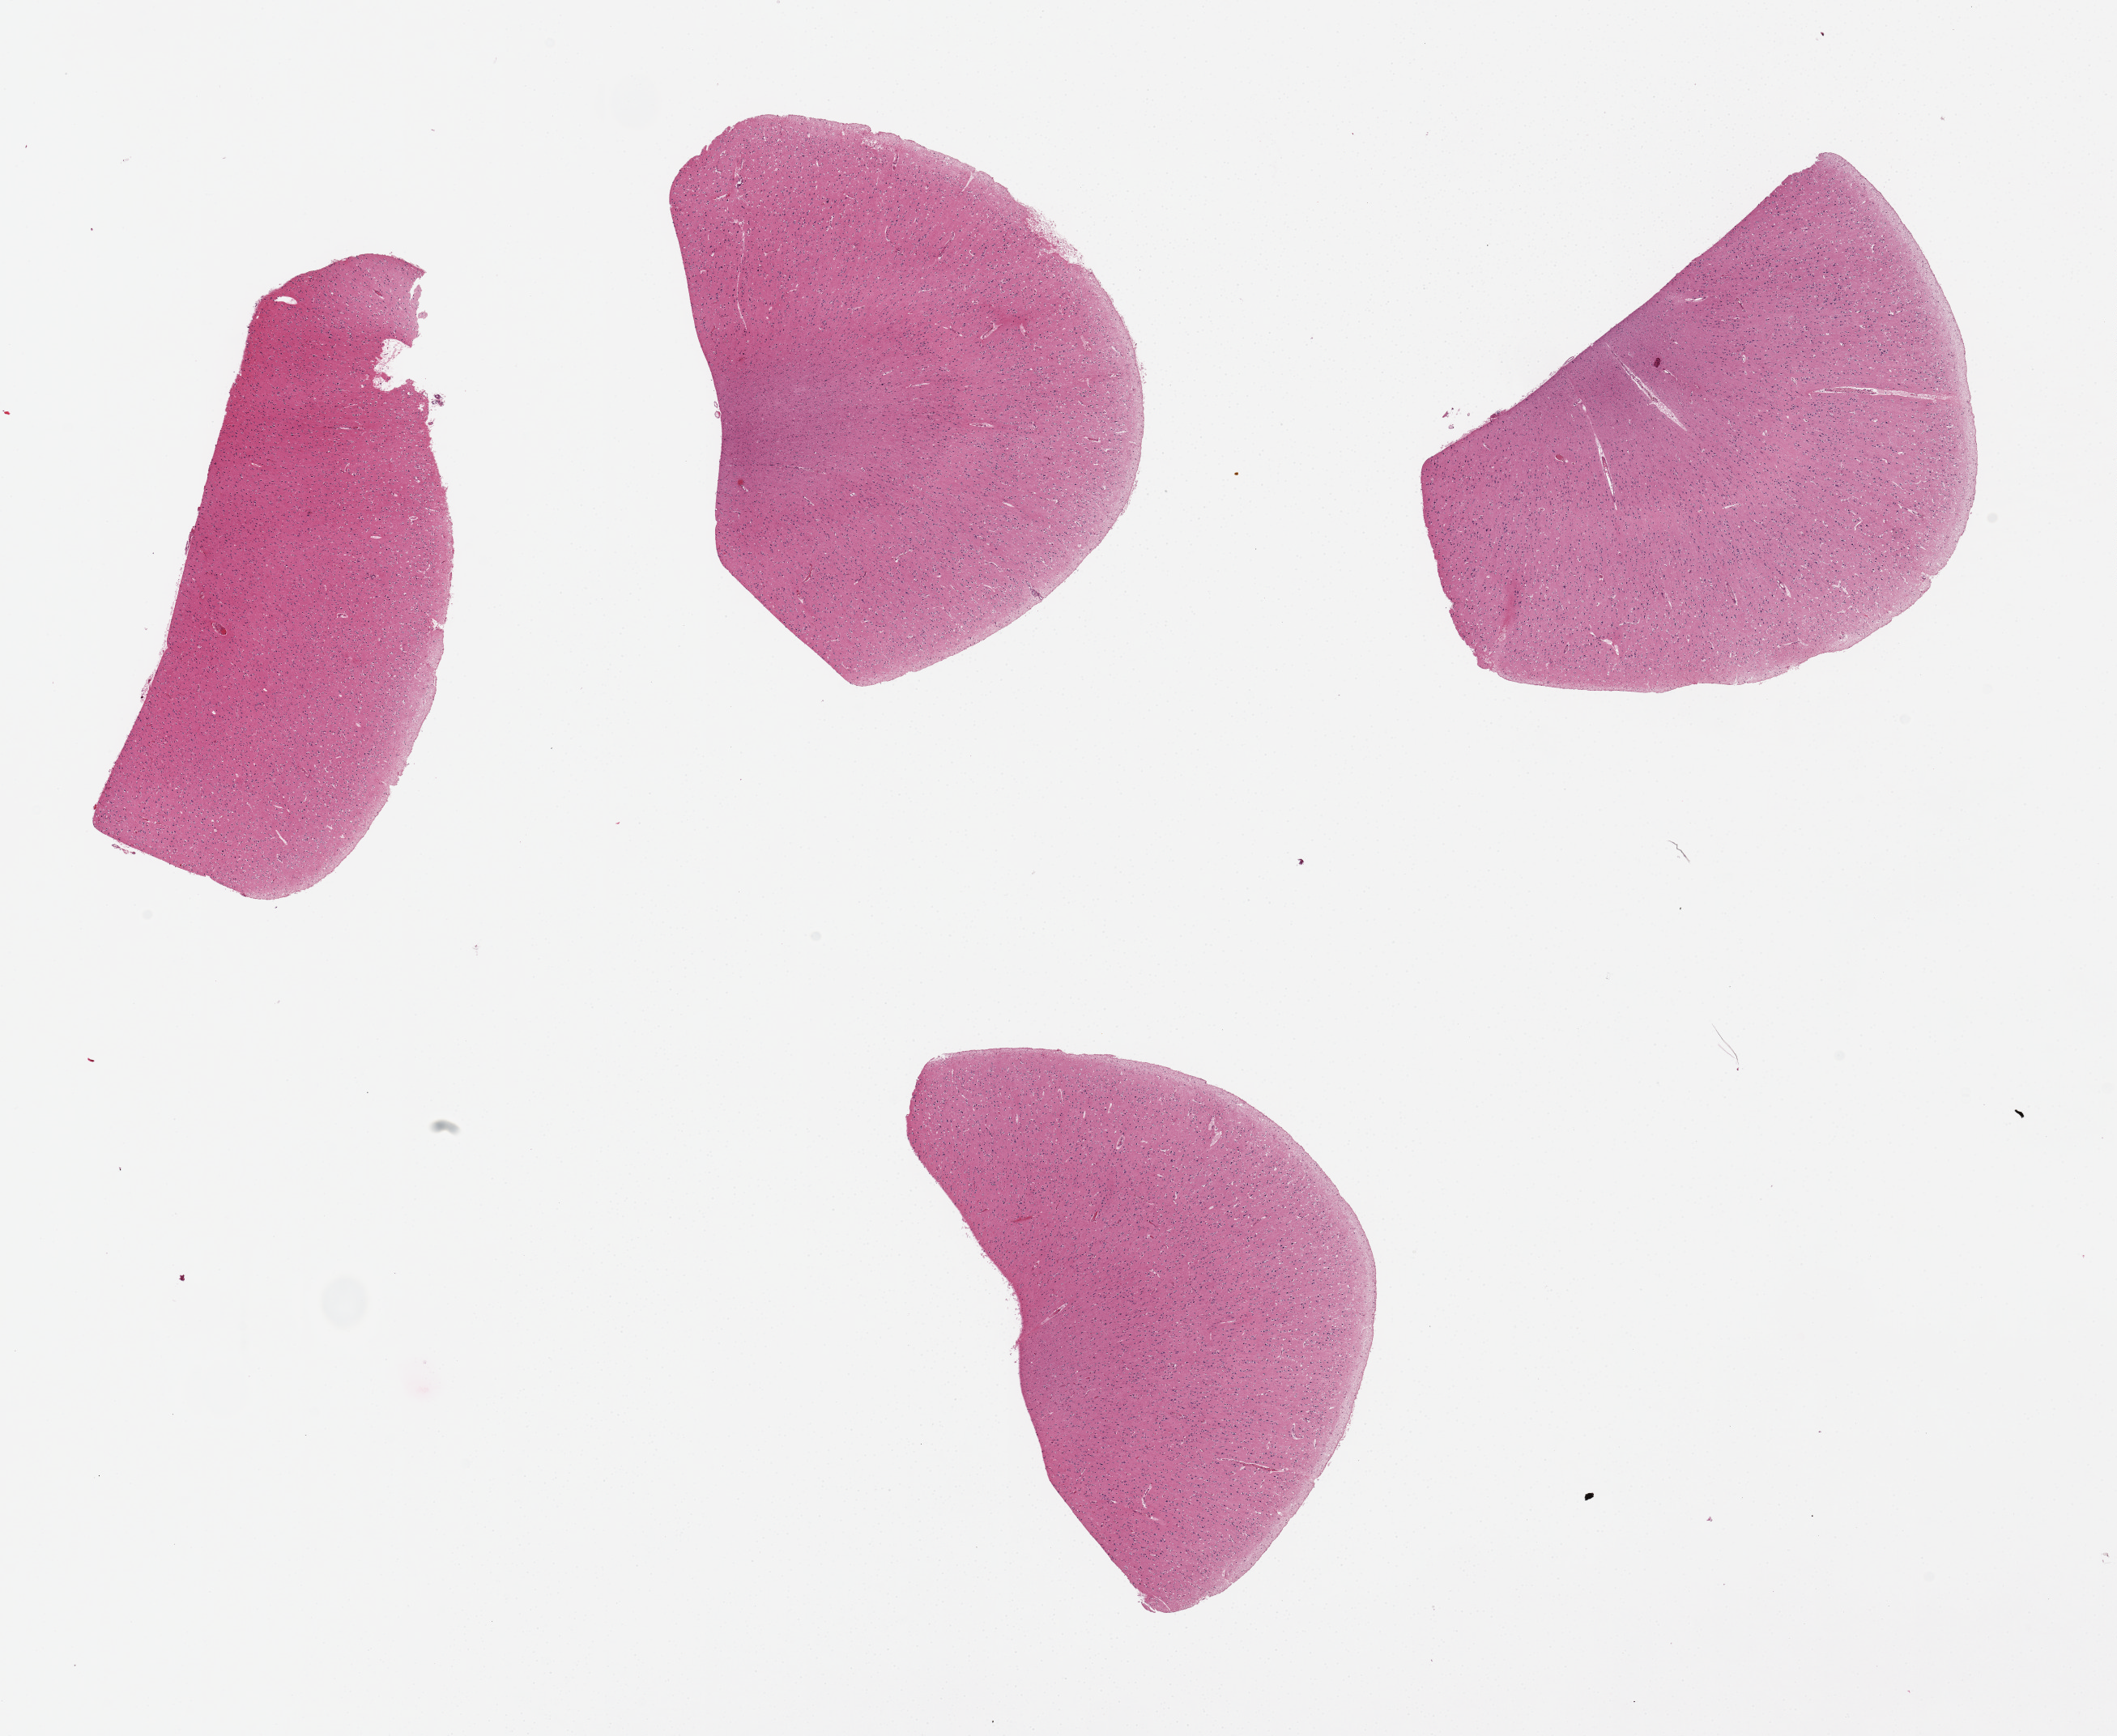
Whole-slide image, H&E stain, brightfield — low-resolution overview of the scanned area, about 20.7 x 17.0 mm (acquisition: 20x scan), PAXgene-fixed, paraffin-embedded tissue, section of cerebral cortex (target tissue), donor tissue sample. Donor sex: female.
Reviewer comment on this tissue sample: 4 pieces.